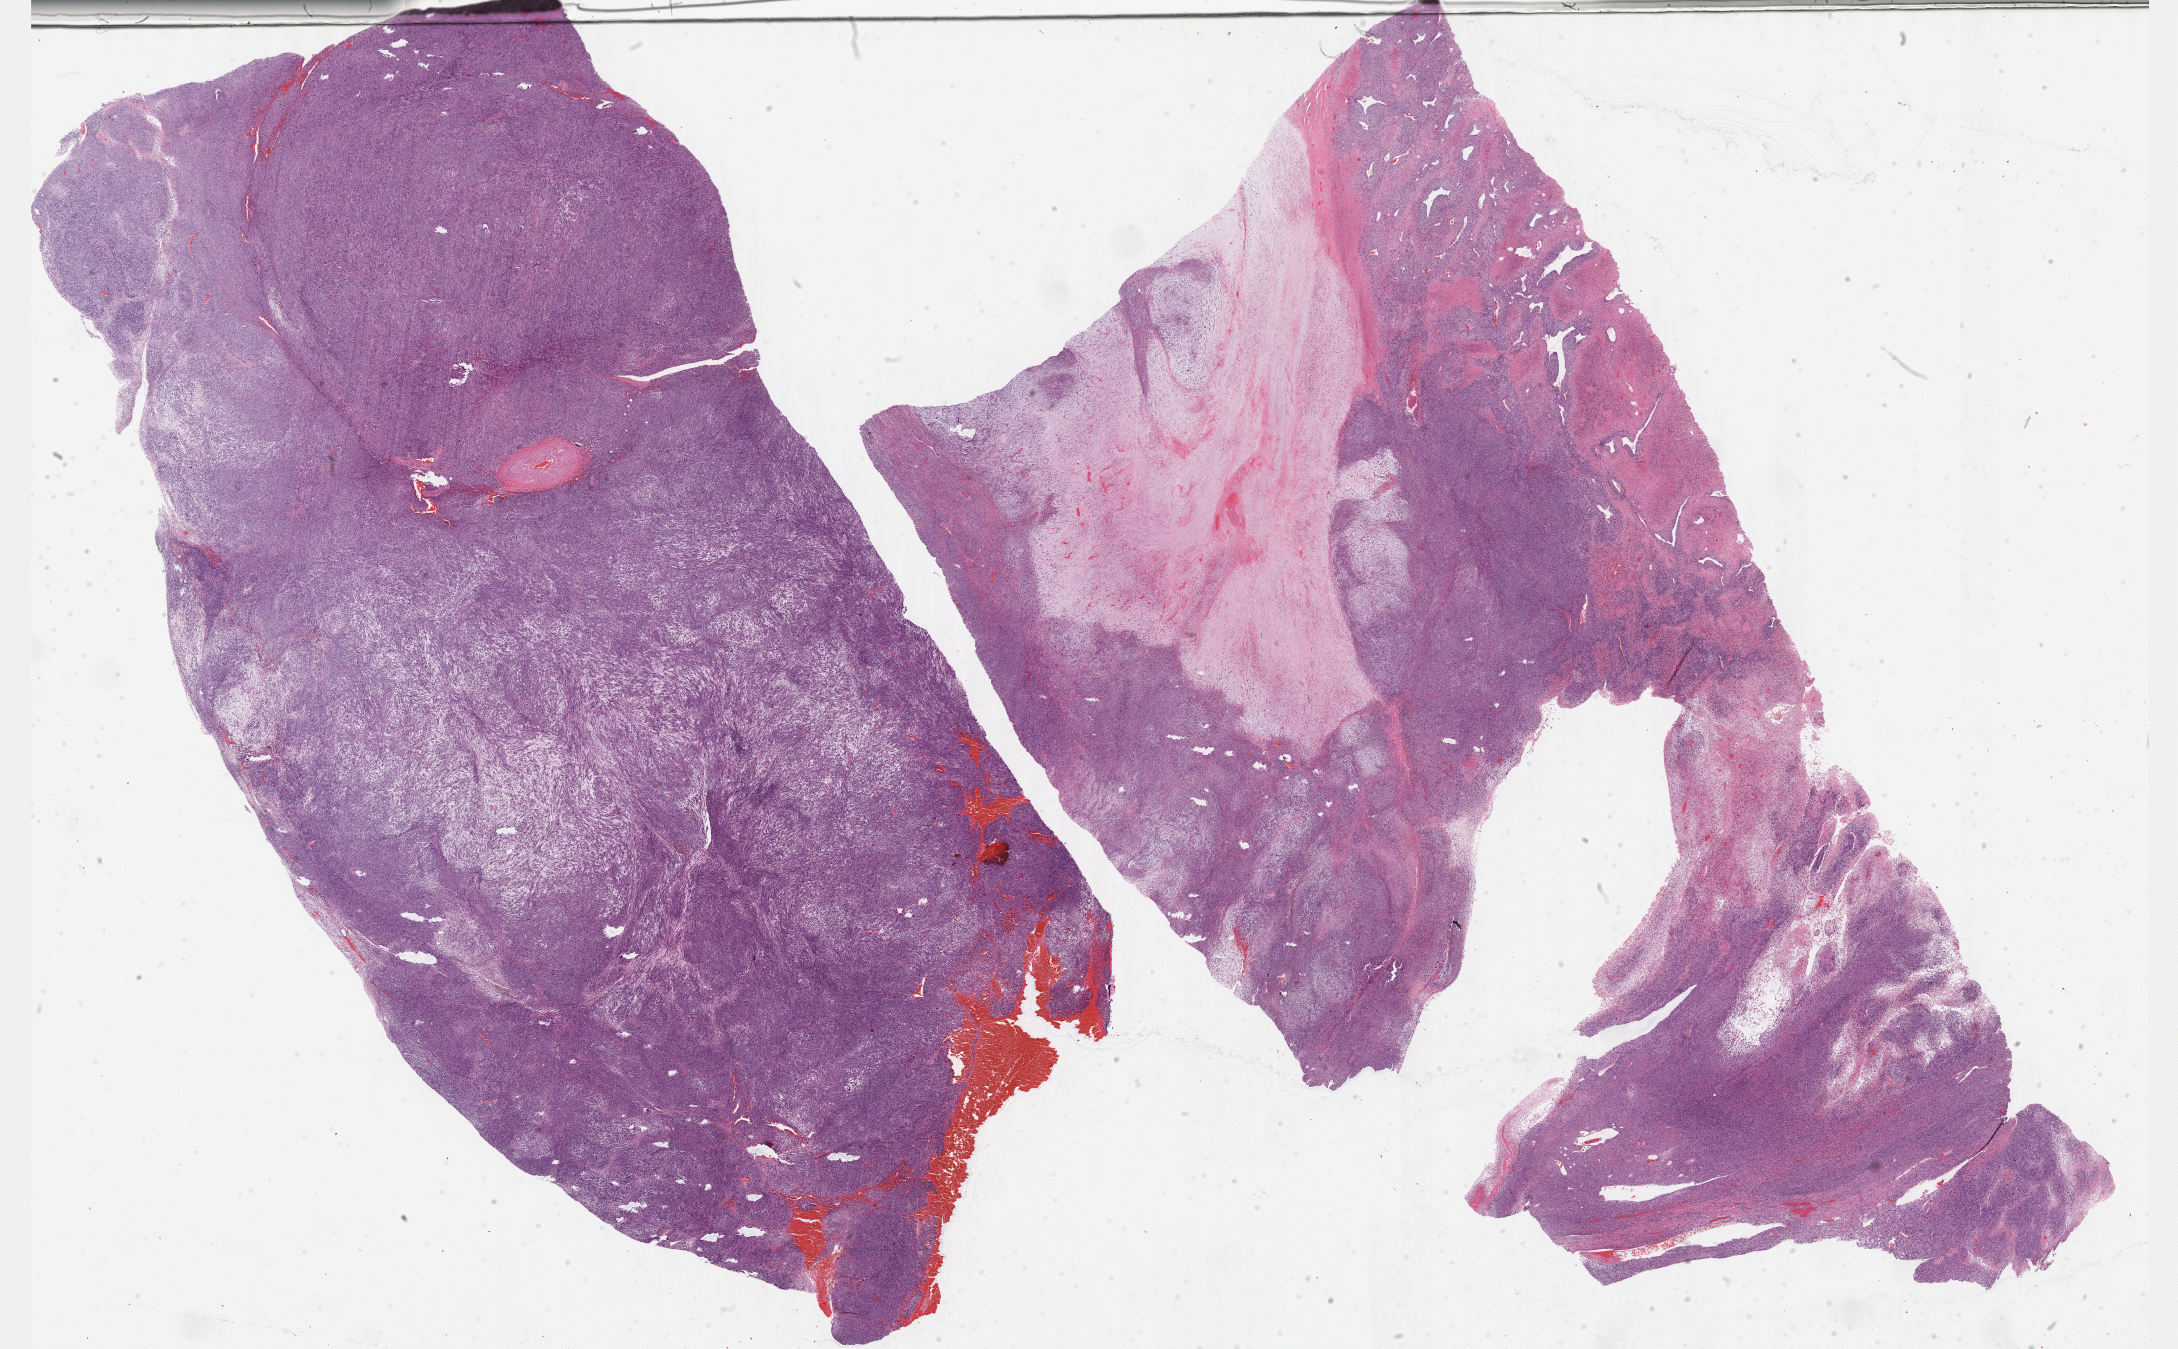
Digitized H&E-stained tissue section (whole slide), shown as a low-resolution overview of the whole scanned area (about 35.2 x 21.8 mm), formalin-fixed paraffin-embedded (FFPE) diagnostic section, primary tumour sample from the connective, subcutaneous and other soft tissues. Female, age 70 years at initial diagnosis.
Diagnosis: Undifferentiated sarcoma (connective, subcutaneous and other soft tissues of lower limb and hip).